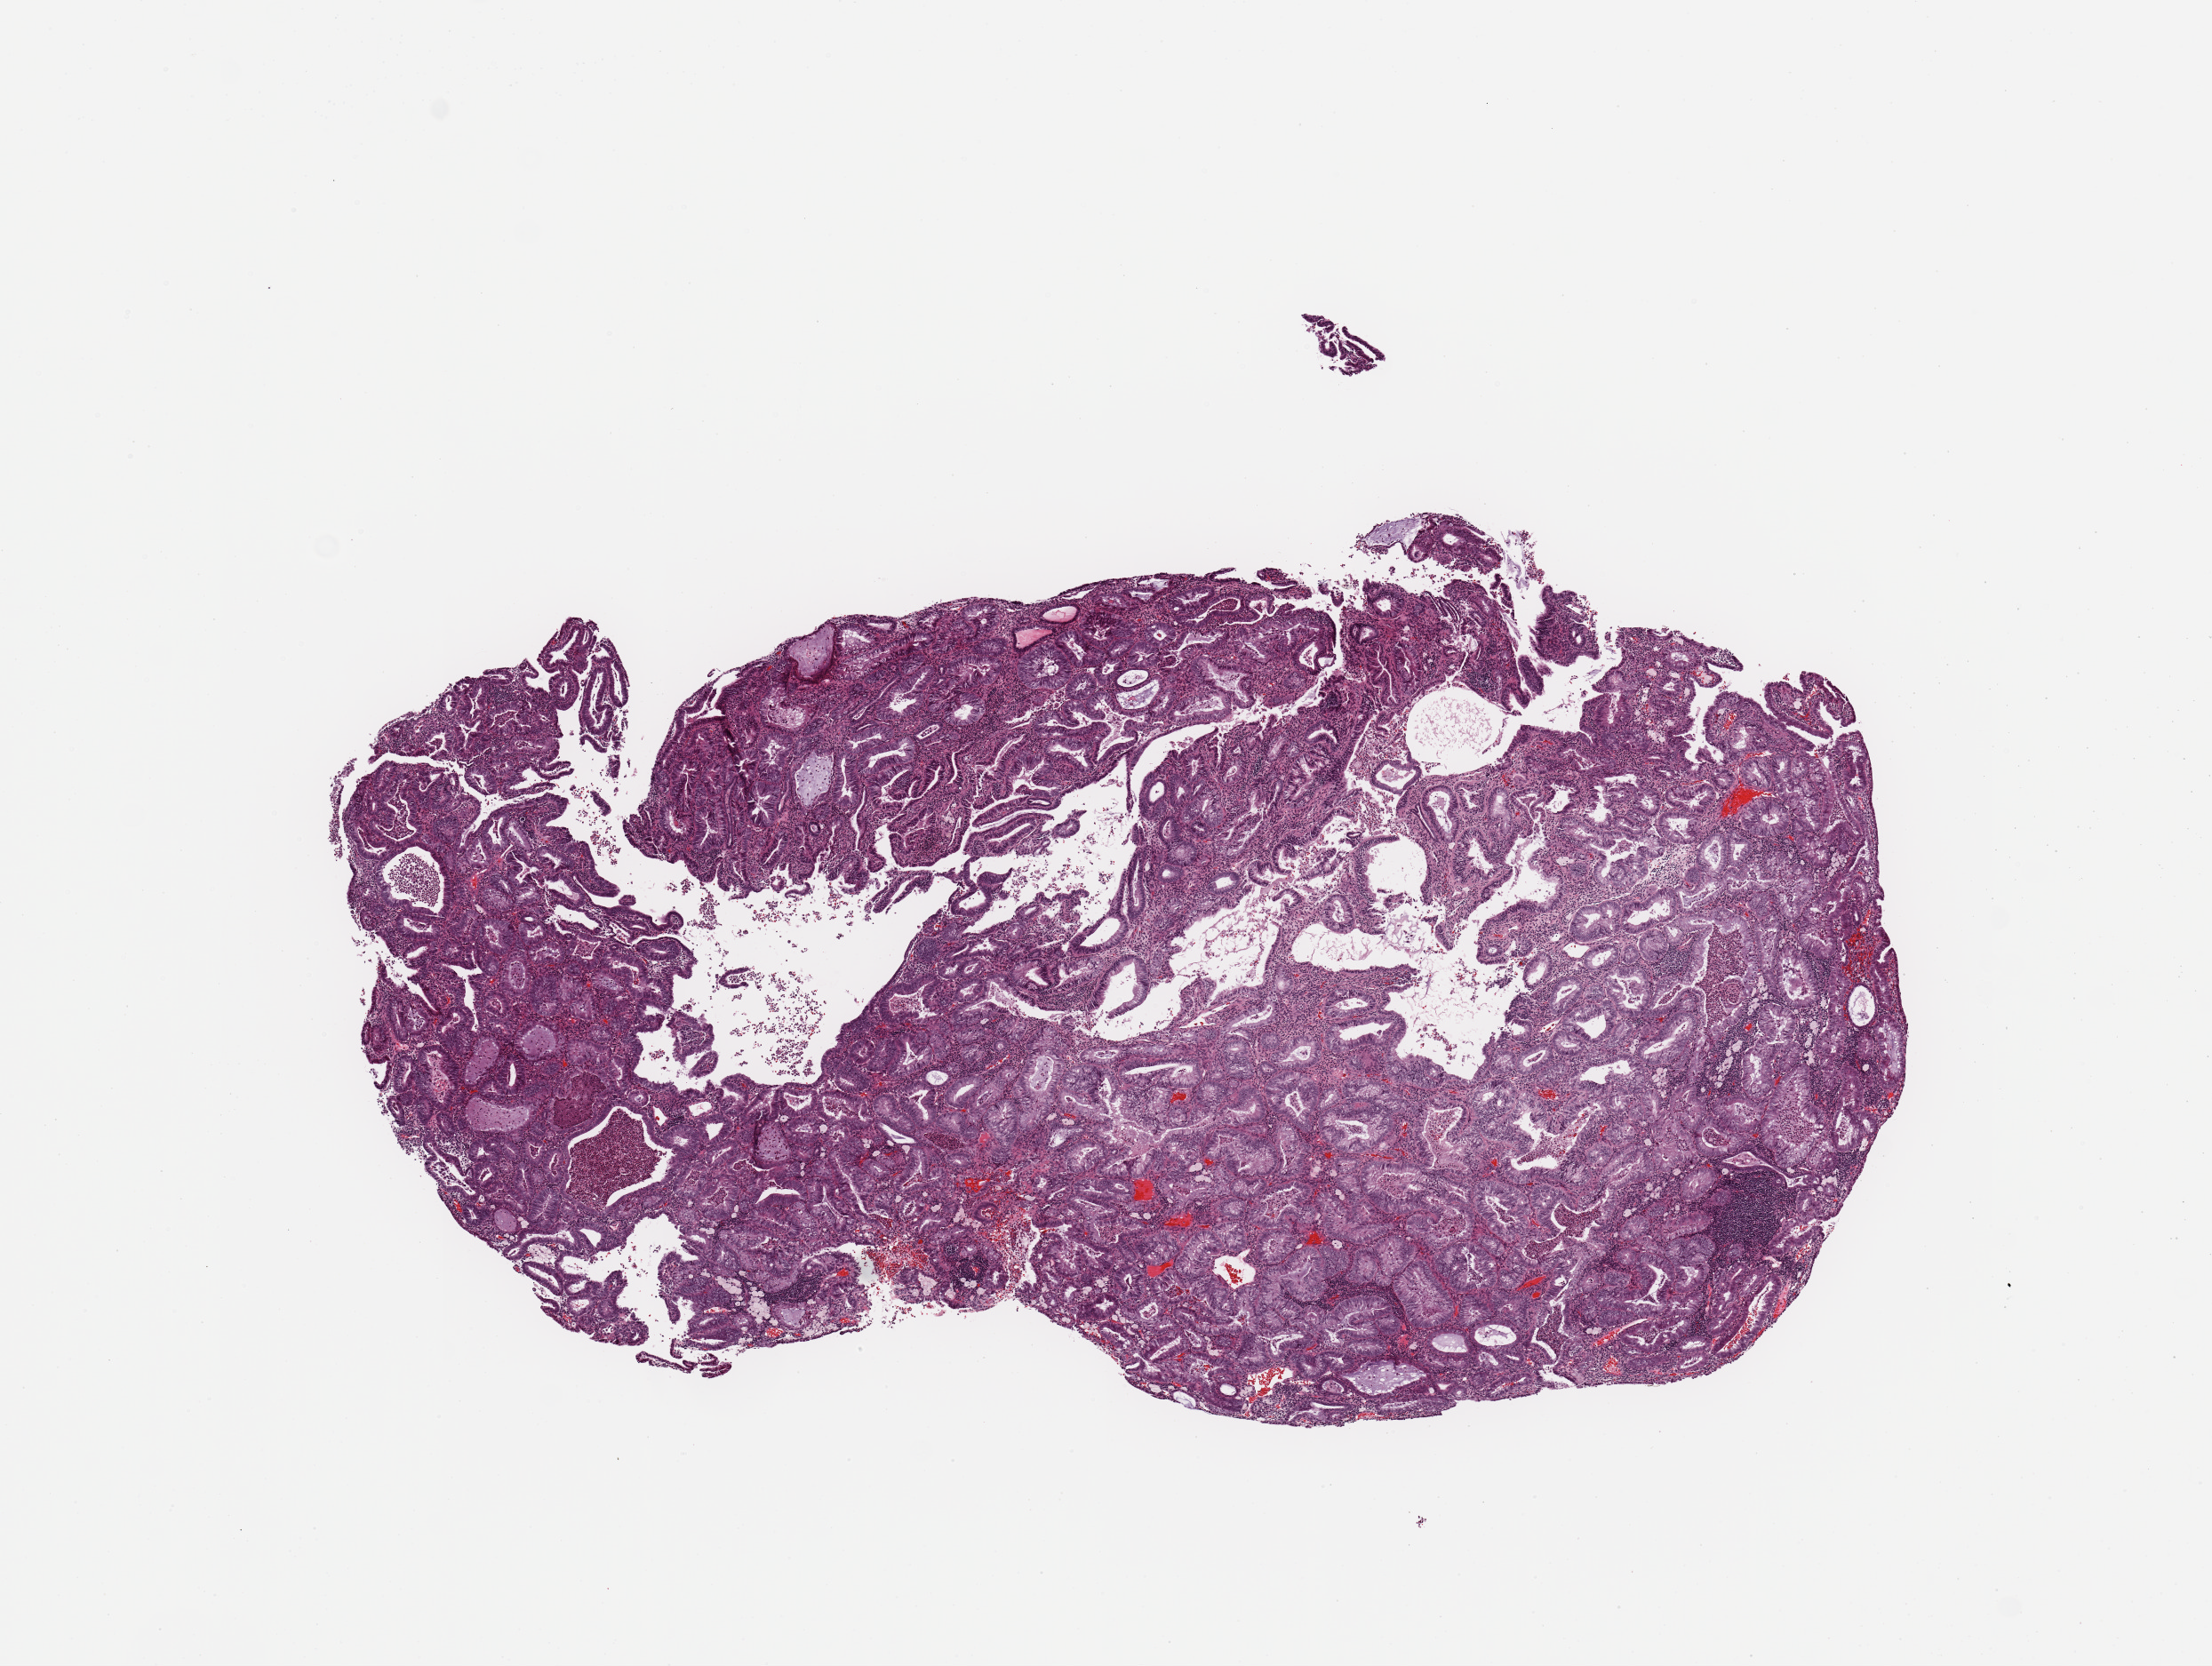
H&E-stained whole-slide image — low-resolution overview of the scanned area, about 9.8 x 7.4 mm (acquisition: 20x scan); tumour tissue sample, sampled site: uterus. Patient: female, age 54 years. Histologic grade: G2 (moderately differentiated). Composition of this section per pathologist review: tumour nuclei 95%, necrosis 2%.
Histologic diagnosis: Endometrioid adenocarcinoma, NOS. AJCC pathologic stage: I.